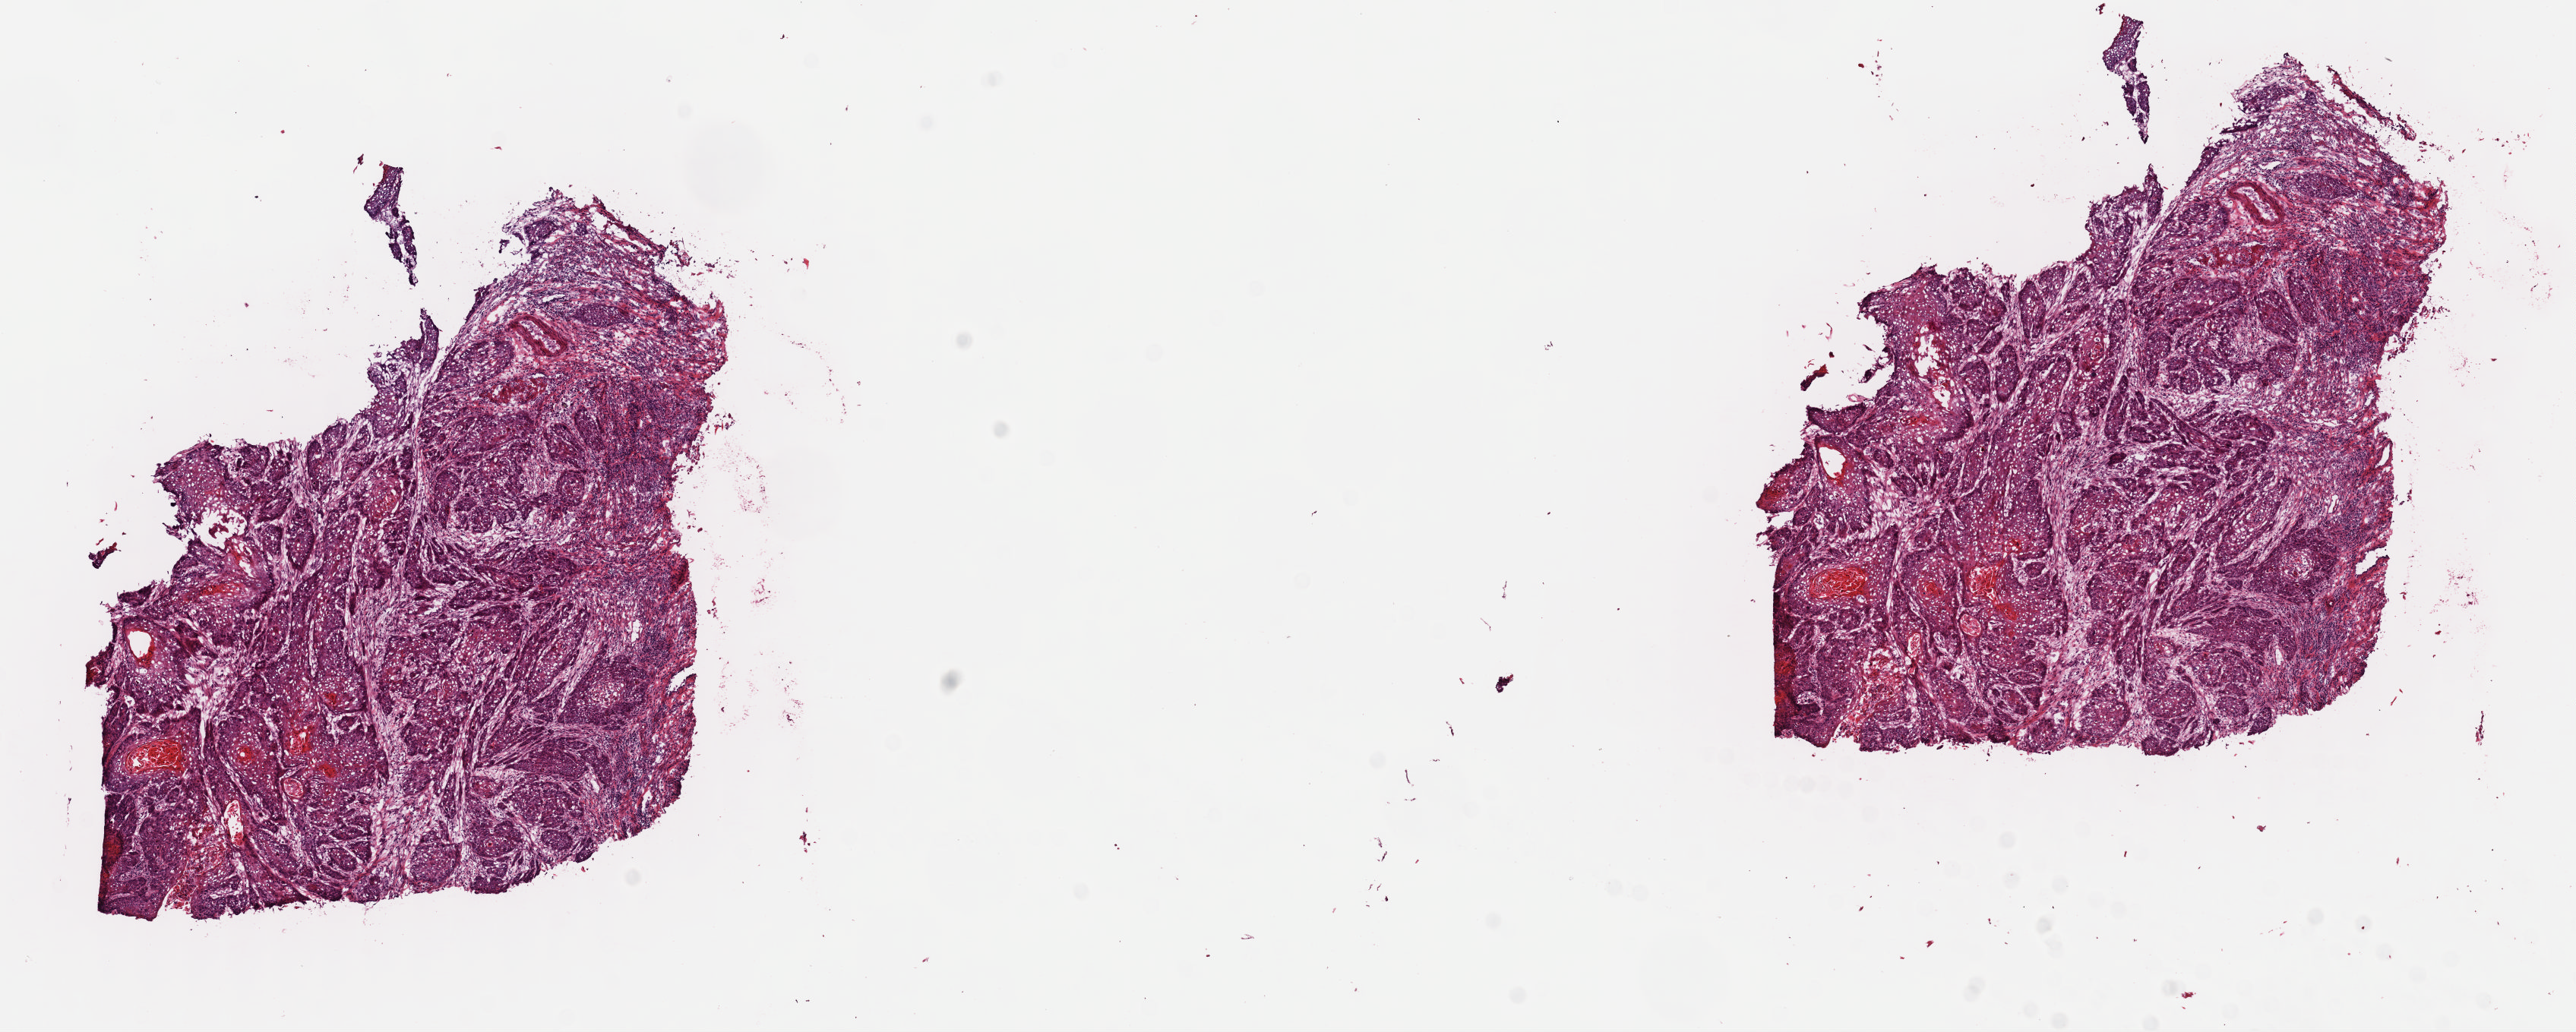
Whole-slide histology image, Hematoxylin and eosin (H&E) stained — a low-resolution overview of the entire scanned area, about 13.4 x 5.4 mm, frozen section from the top of the tissue portion, primary tumour sample from the cervix. Female, age 26 years at initial diagnosis. Histologic grade: G2 (moderately differentiated). Pathologist review of this section (percent, as recorded): tumour cells 70%, tumour nuclei 70%, normal cells 10%, stromal cells 19%, necrosis 1%. Infiltration values recorded for this section: lymphocyte infiltration 20%, monocyte infiltration 0%, neutrophil infiltration 4%.
FIGO stage: IIA. Pathologic diagnosis: Squamous cell carcinoma, keratinizing, NOS (cervix uteri).